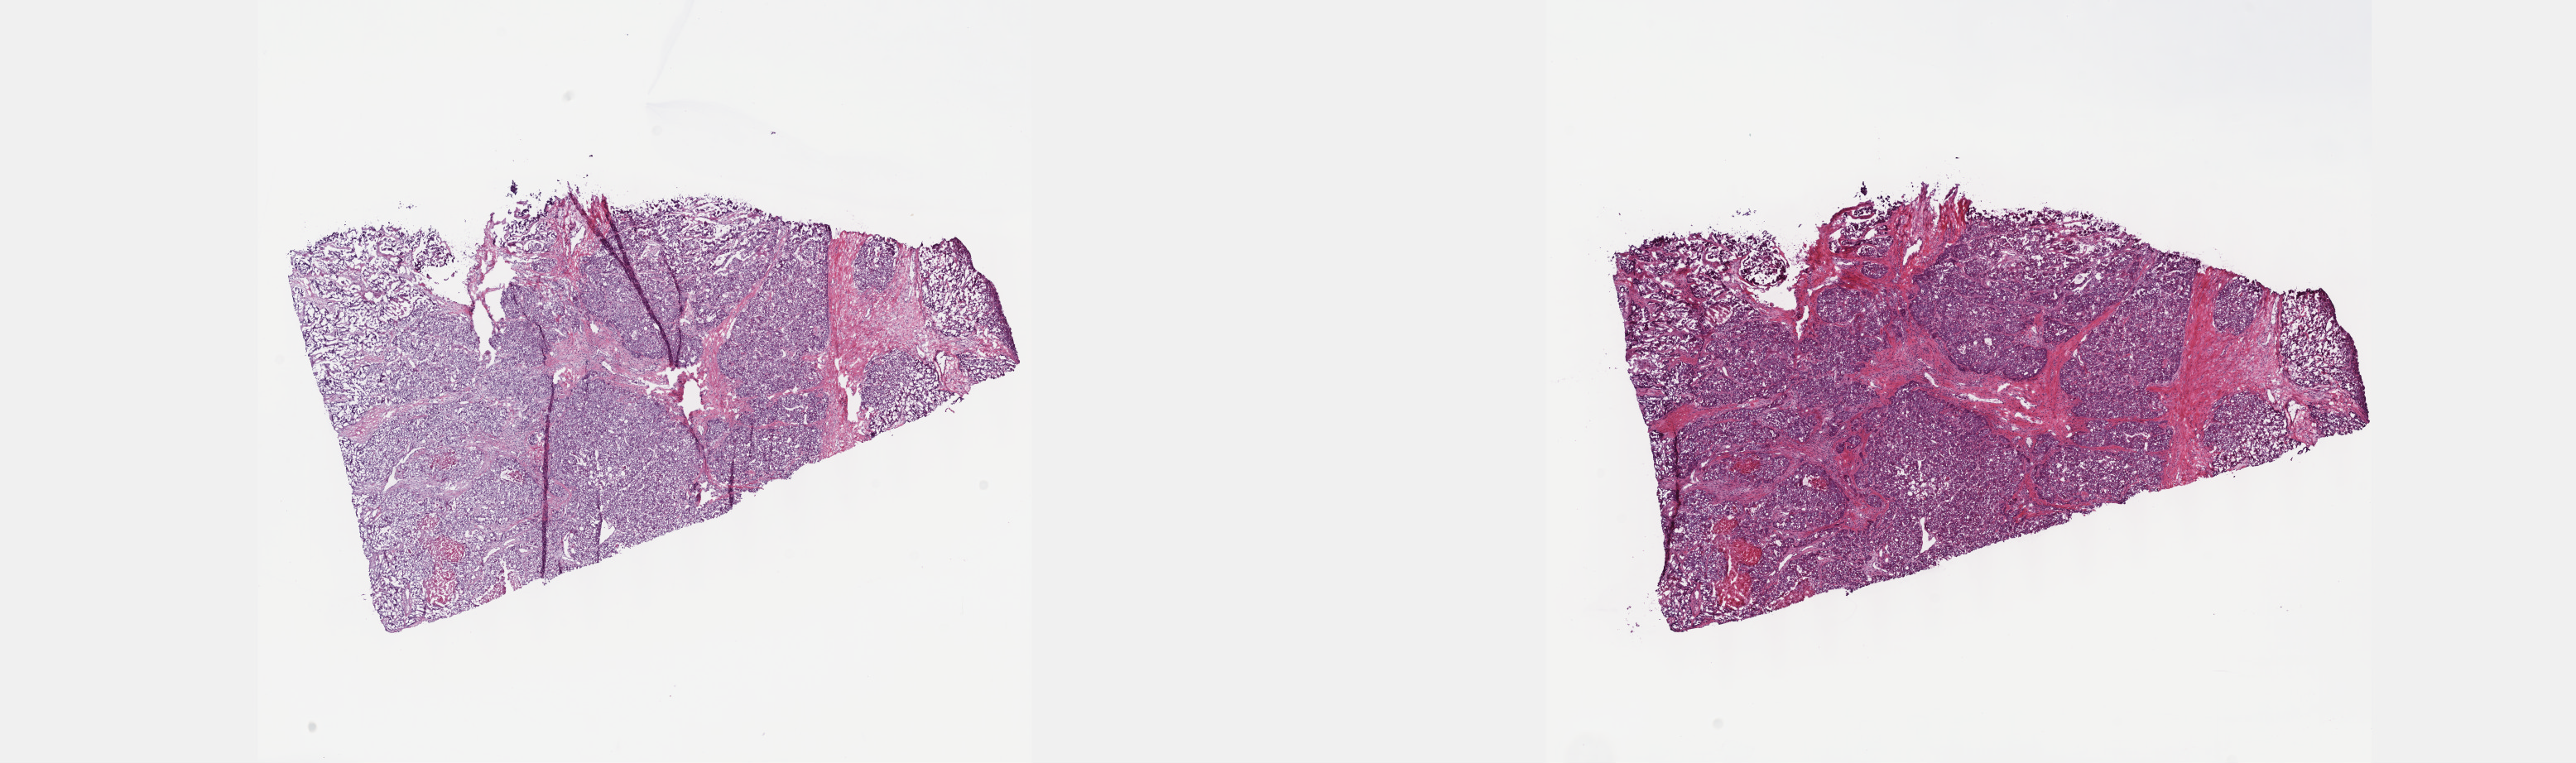
Digitized H&E tissue section (whole slide) — a low-resolution overview of the entire scanned area, about 25.1 x 7.5 mm (from a 40x scan). Frozen section from the top of the tissue portion. Bile duct, primary tumour sample. Patient: female, age at initial diagnosis 55 years. Histologic grade: G3 (poorly differentiated). Slide review estimates, as recorded: tumour cells 75%, tumour nuclei 80%, normal cells 0%, stromal cells 25%, necrosis 0%. Infiltration values recorded for this section: lymphocyte infiltration 0%, monocyte infiltration 0%, neutrophil infiltration 0%.
* histologic diagnosis: Cholangiocarcinoma (intrahepatic bile duct)
* TNM: T1 N0 M0
* AJCC pathologic stage: I (7th edition)